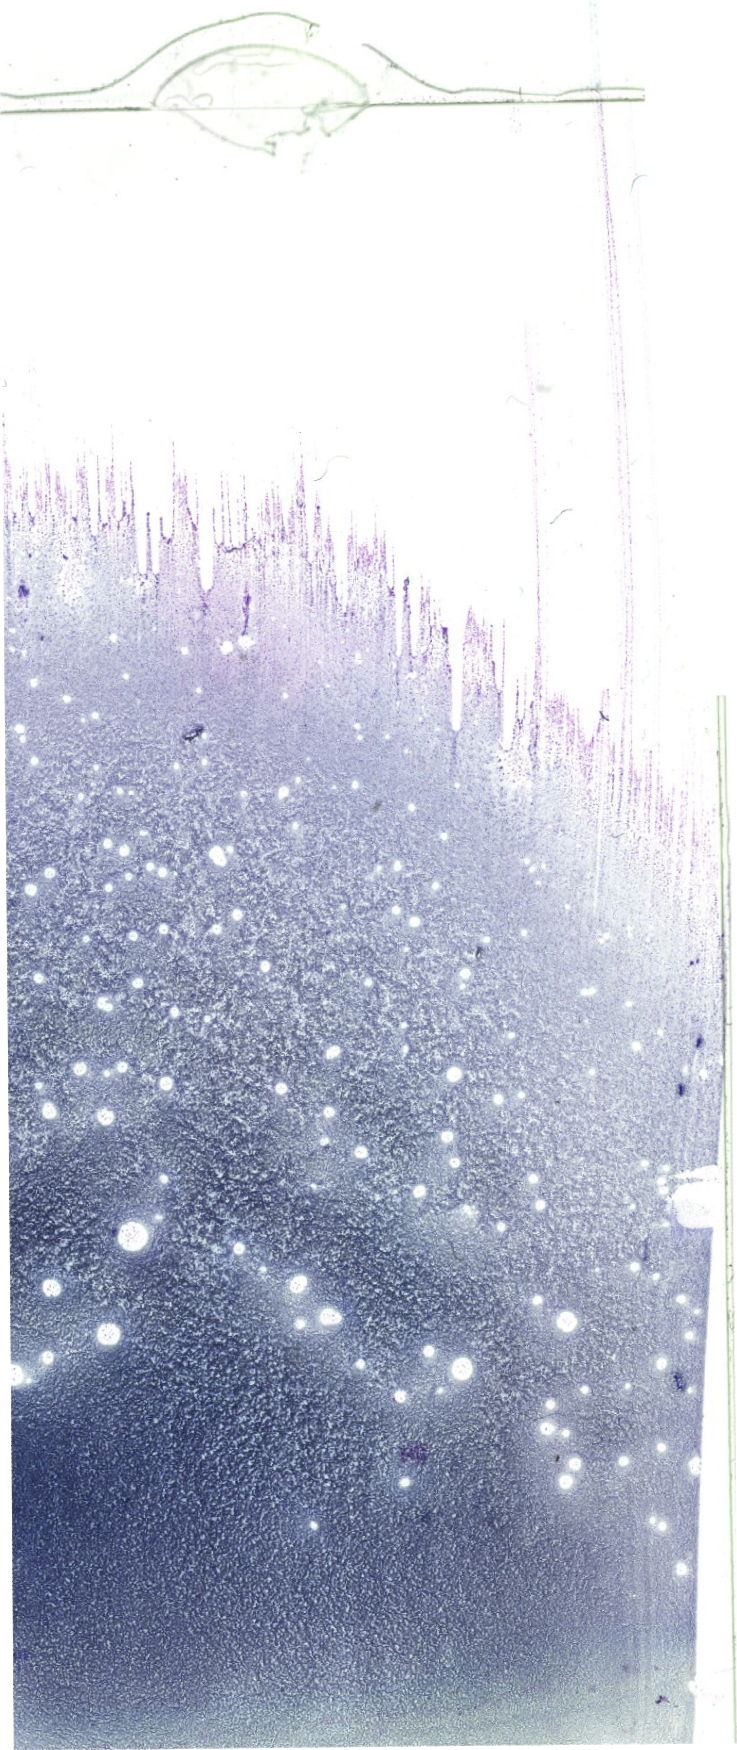
Bone marrow aspirate smear, May-Grünwald–Giemsa stain, whole-slide image — low-resolution overview of the scanned area, about 20.9 x 49.6 mm. Patient sex: male.
Diagnosis: T Acute Lymphoblastic Leukemia.